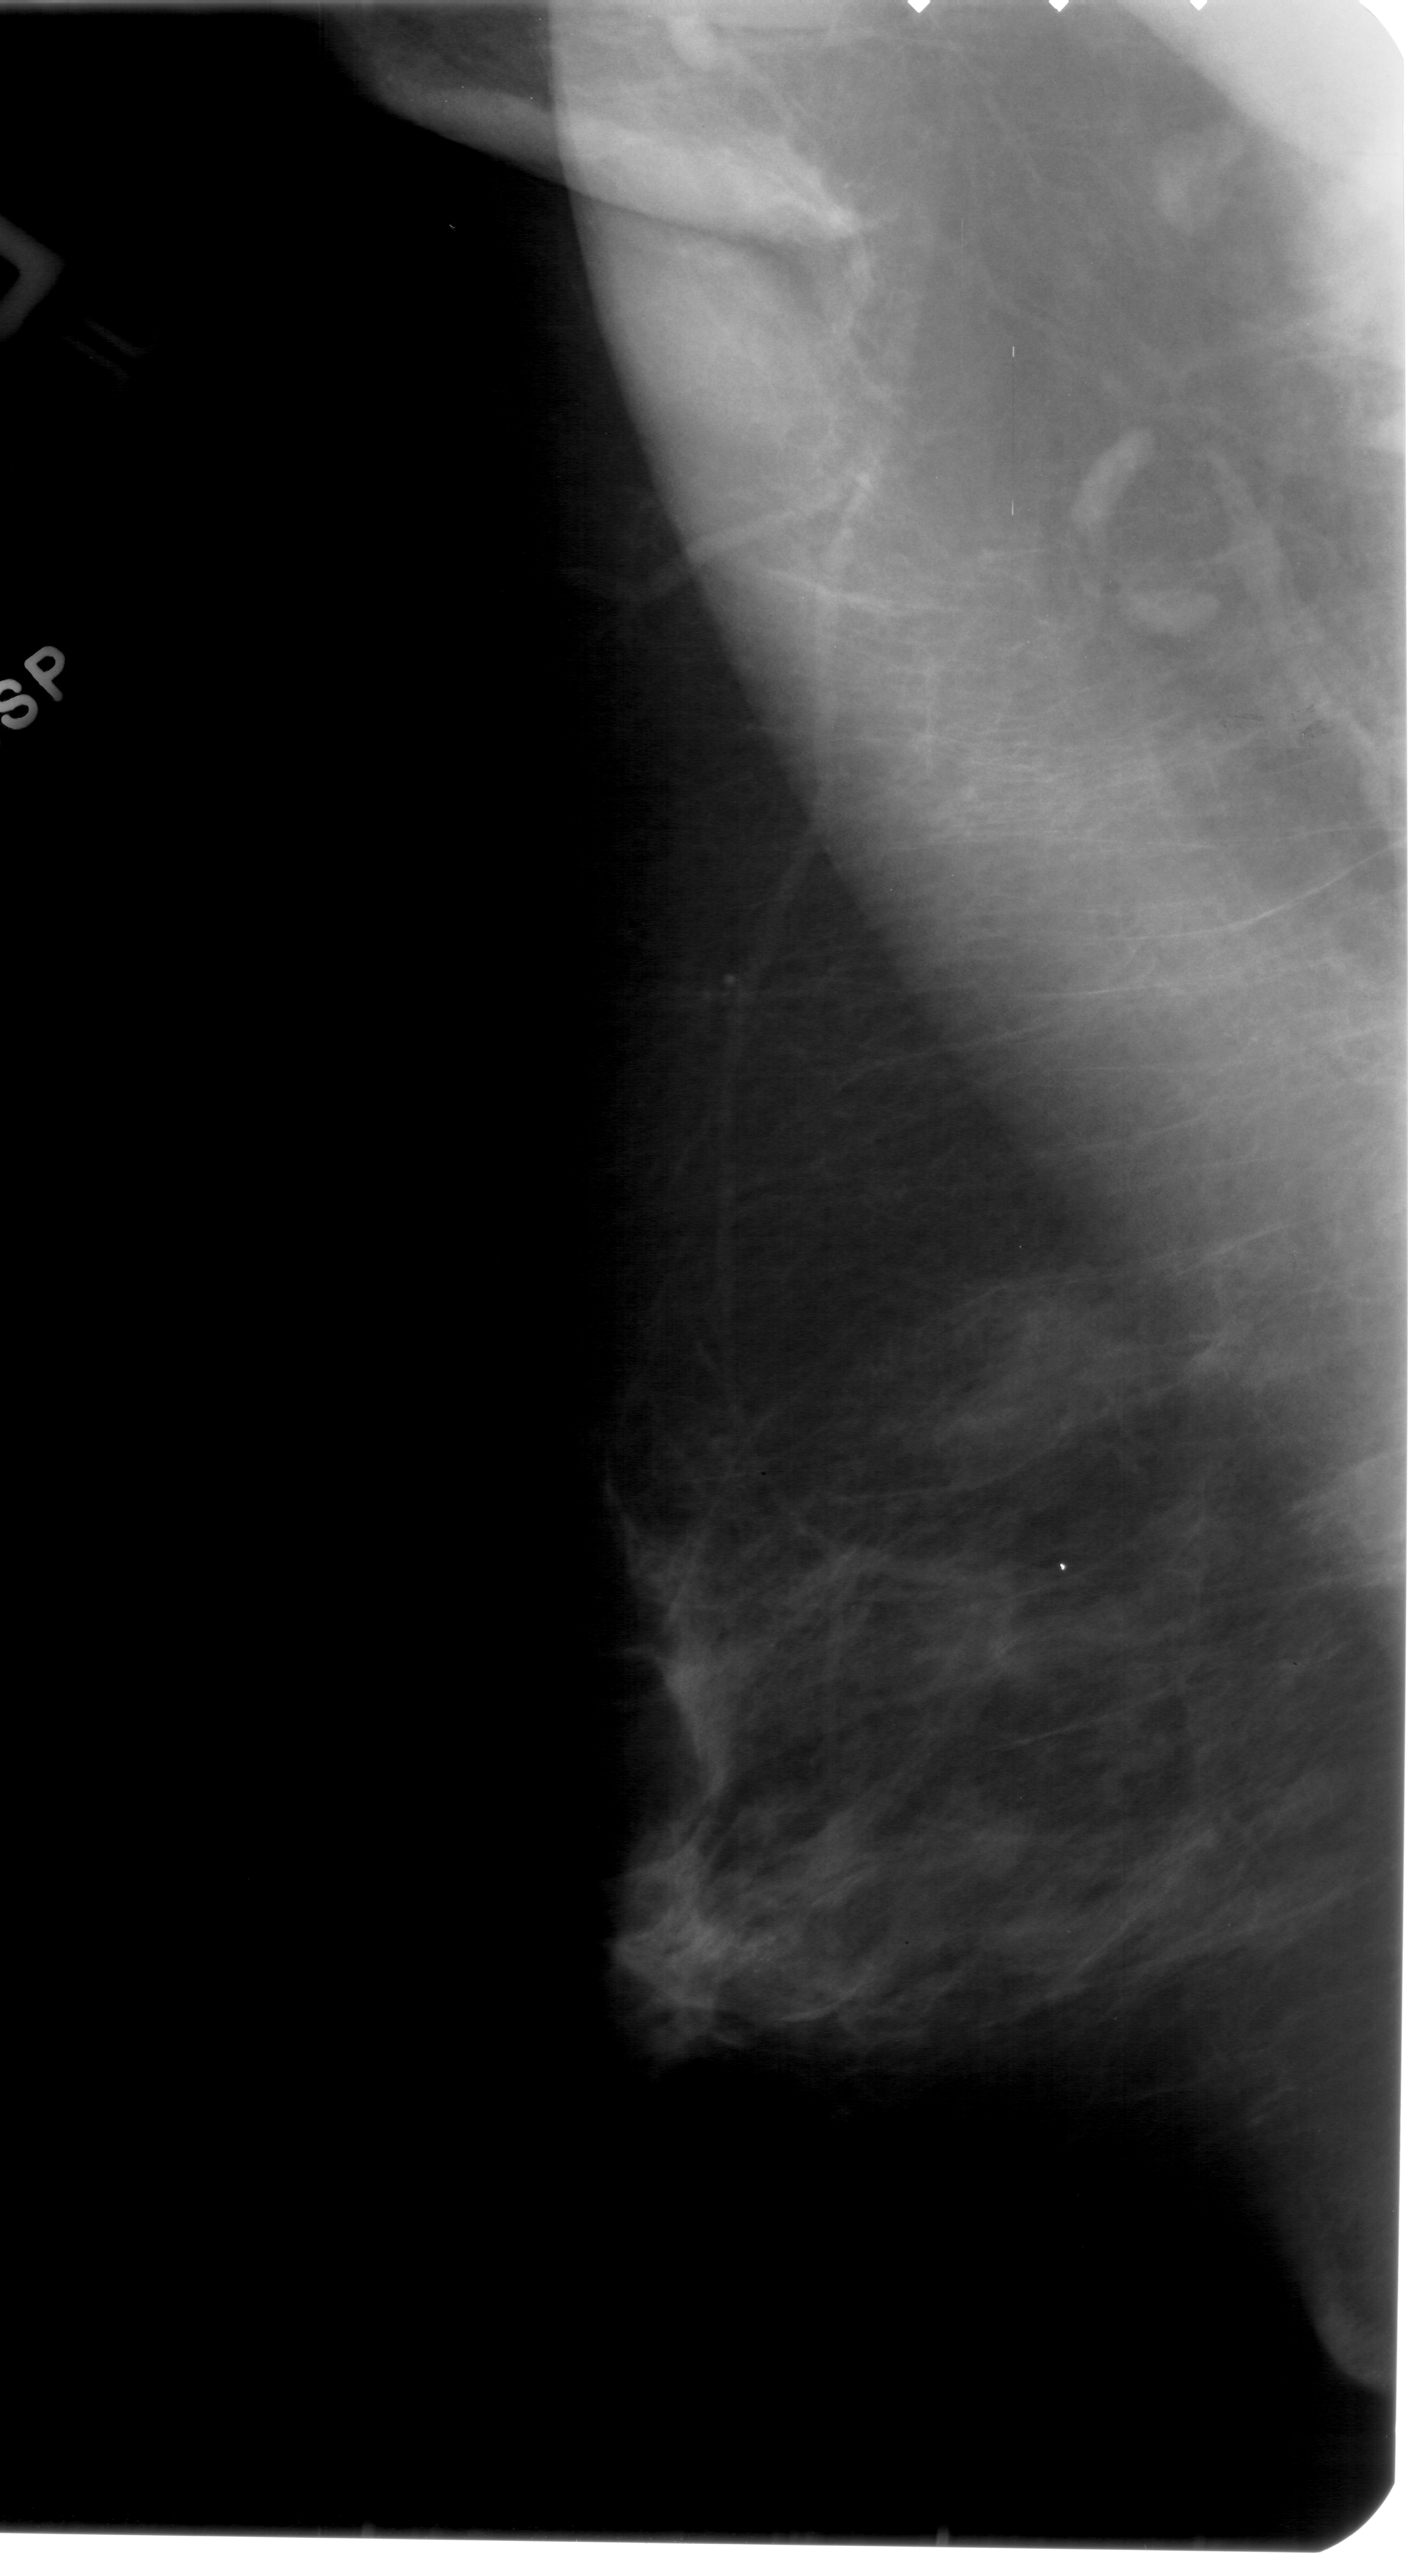
Scanned film-screen mammogram. Left breast. MLO view. Breast composition: scattered fibroglandular densities (BI-RADS density category 2 of 4). 1408 × 2576 image matrix.
Expert-marked regions of interest on this image (one box per marked abnormality):
- calcifications, morphology pleomorphic, distribution clustered; BI-RADS assessment category 4; pathology result (as recorded, not read from the image): benign: bounding box [x1, y1, x2, y2] px = [660, 1923, 807, 1999]